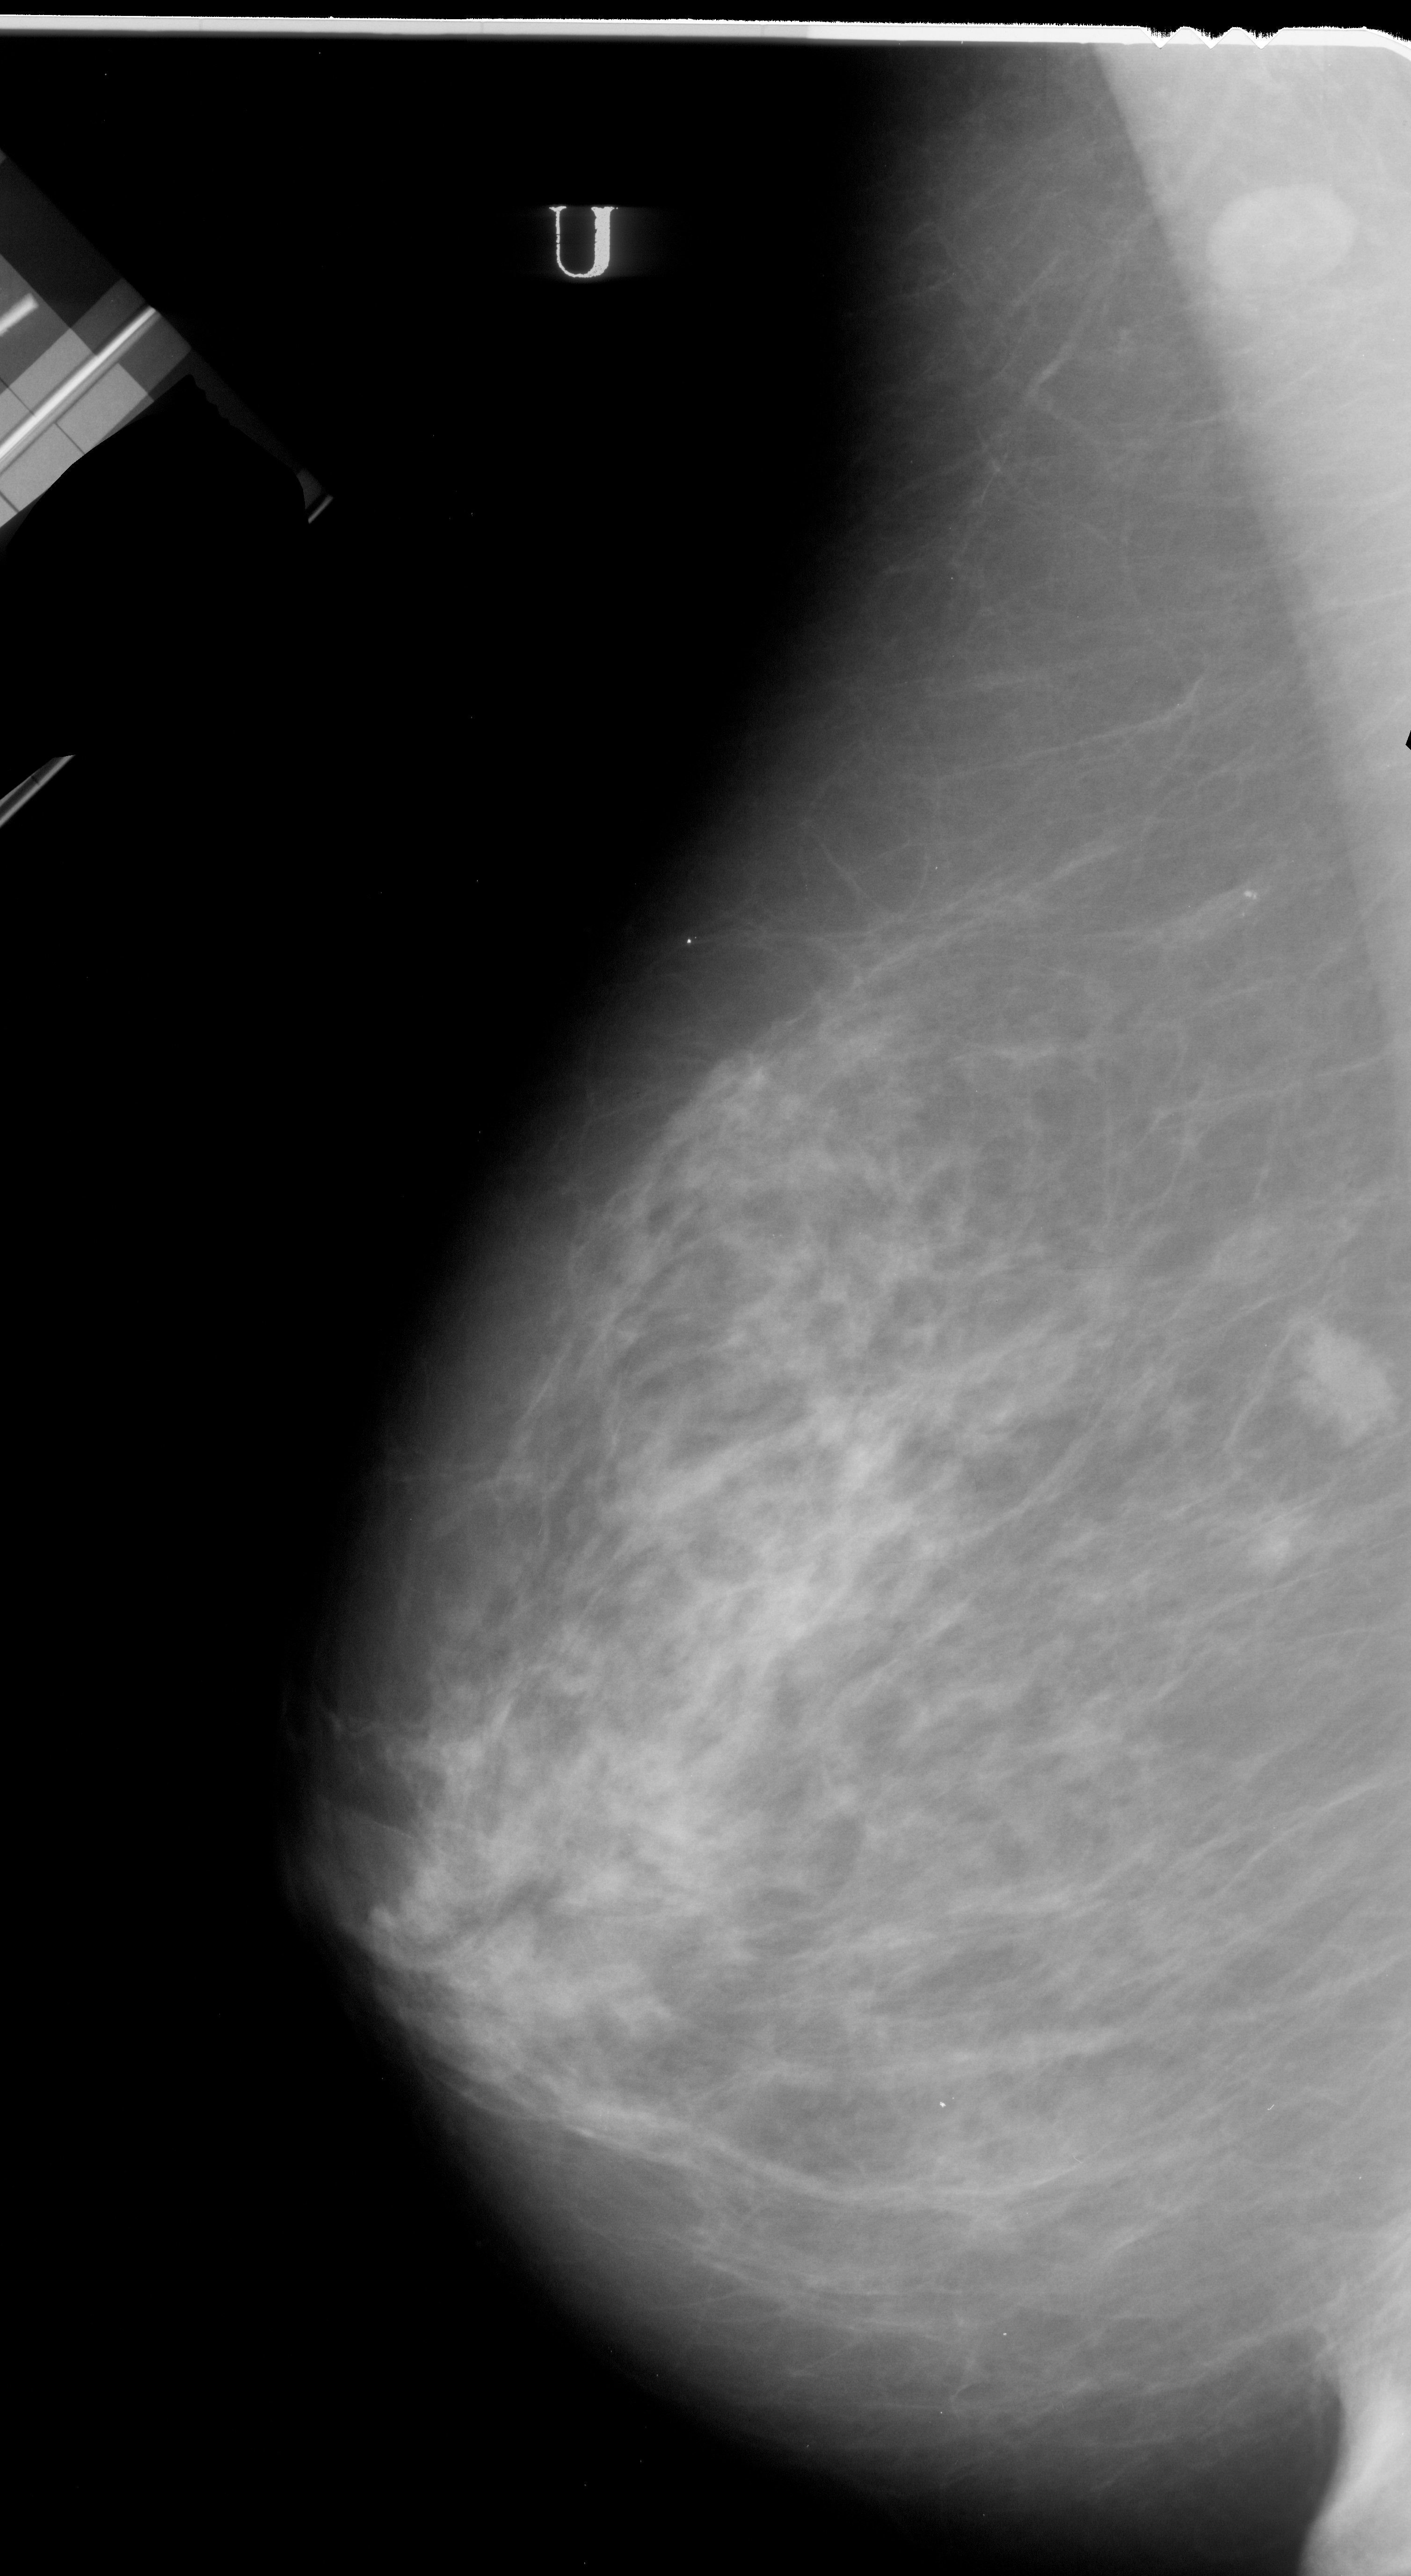
Digitized screen-film mammogram; left breast; mediolateral oblique (MLO) view; breast composition: heterogeneously dense (BI-RADS density category 3 of 4); 1411 × 2576 image matrix.
Marked abnormalities (boxes around the expert regions of interest):
- mass, shape irregular, margins spiculated; BI-RADS assessment category 5; pathology (as recorded): malignant: box from (x=1284, y=1322) to (x=1396, y=1443) px